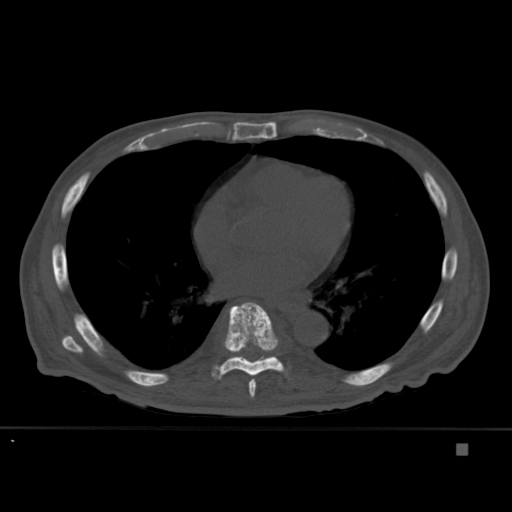
CT including the spine, one axial slice; slice 264 of 451 in the series (ordered by position); bone window (W 1800 / L 400 HU); 1.5 mm slice thickness; 512 × 512 image matrix, field of view 378 × 378 mm. Patient: male, 75 years. From the clinical record (not read from this slice): primary cancer: prostate.
Outlined on this slice (semi-automatically segmented with operator editing):
- T7 vertebra: bounding box [x1, y1, x2, y2] px = [249, 378, 257, 399]
- T8 vertebra: [212, 302, 287, 380]
- T9 vertebra: [234, 356, 275, 361]